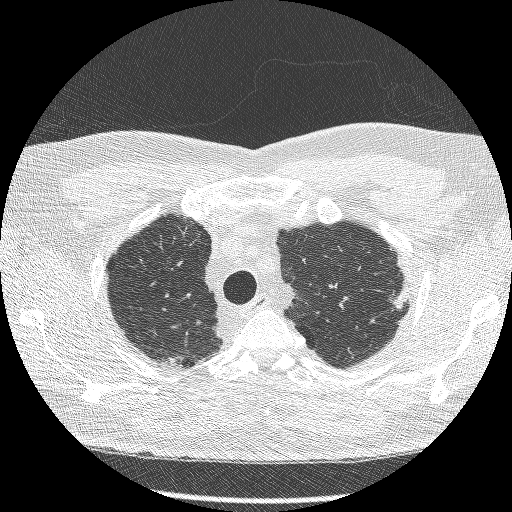
Axial slice from a low-dose chest CT screening exam, second annual screen, lung window (W 1500 / L -600 HU), 1.25 mm slice thickness, lung (sharp) reconstruction kernel (BONE), slice 228 of 269 in the series, 512 × 512 image matrix. Male participant, aged 66 years at enrolment. Current smoker at enrolment.
• Lesion marked by an expert reader, box from (x=382, y=272) to (x=421, y=320) px.
• The exam's reader record, not a measurement of the box and not confirmed to be the same lesion: non-calcified nodule or mass ≥4 mm, right lower lobe, 40 × 19 mm, spiculated (stellate) margins, soft tissue attenuation, pre-existing on the prior screen: yes; interval growth: no.
• Note: the box lies in the patient's left hemithorax on this image, whereas the reader's record names the right lung; they may be different findings.
• Official screen result: negative screen, minor abnormalities not suspicious for lung cancer.
• Later outcome: lung cancer diagnosed 554 days after this screen (after the third annual screen) — adenocarcinoma, NOS, left upper lobe, poorly differentiated (G3), stage IB (AJCC 6th edition), 16 mm at pathology.